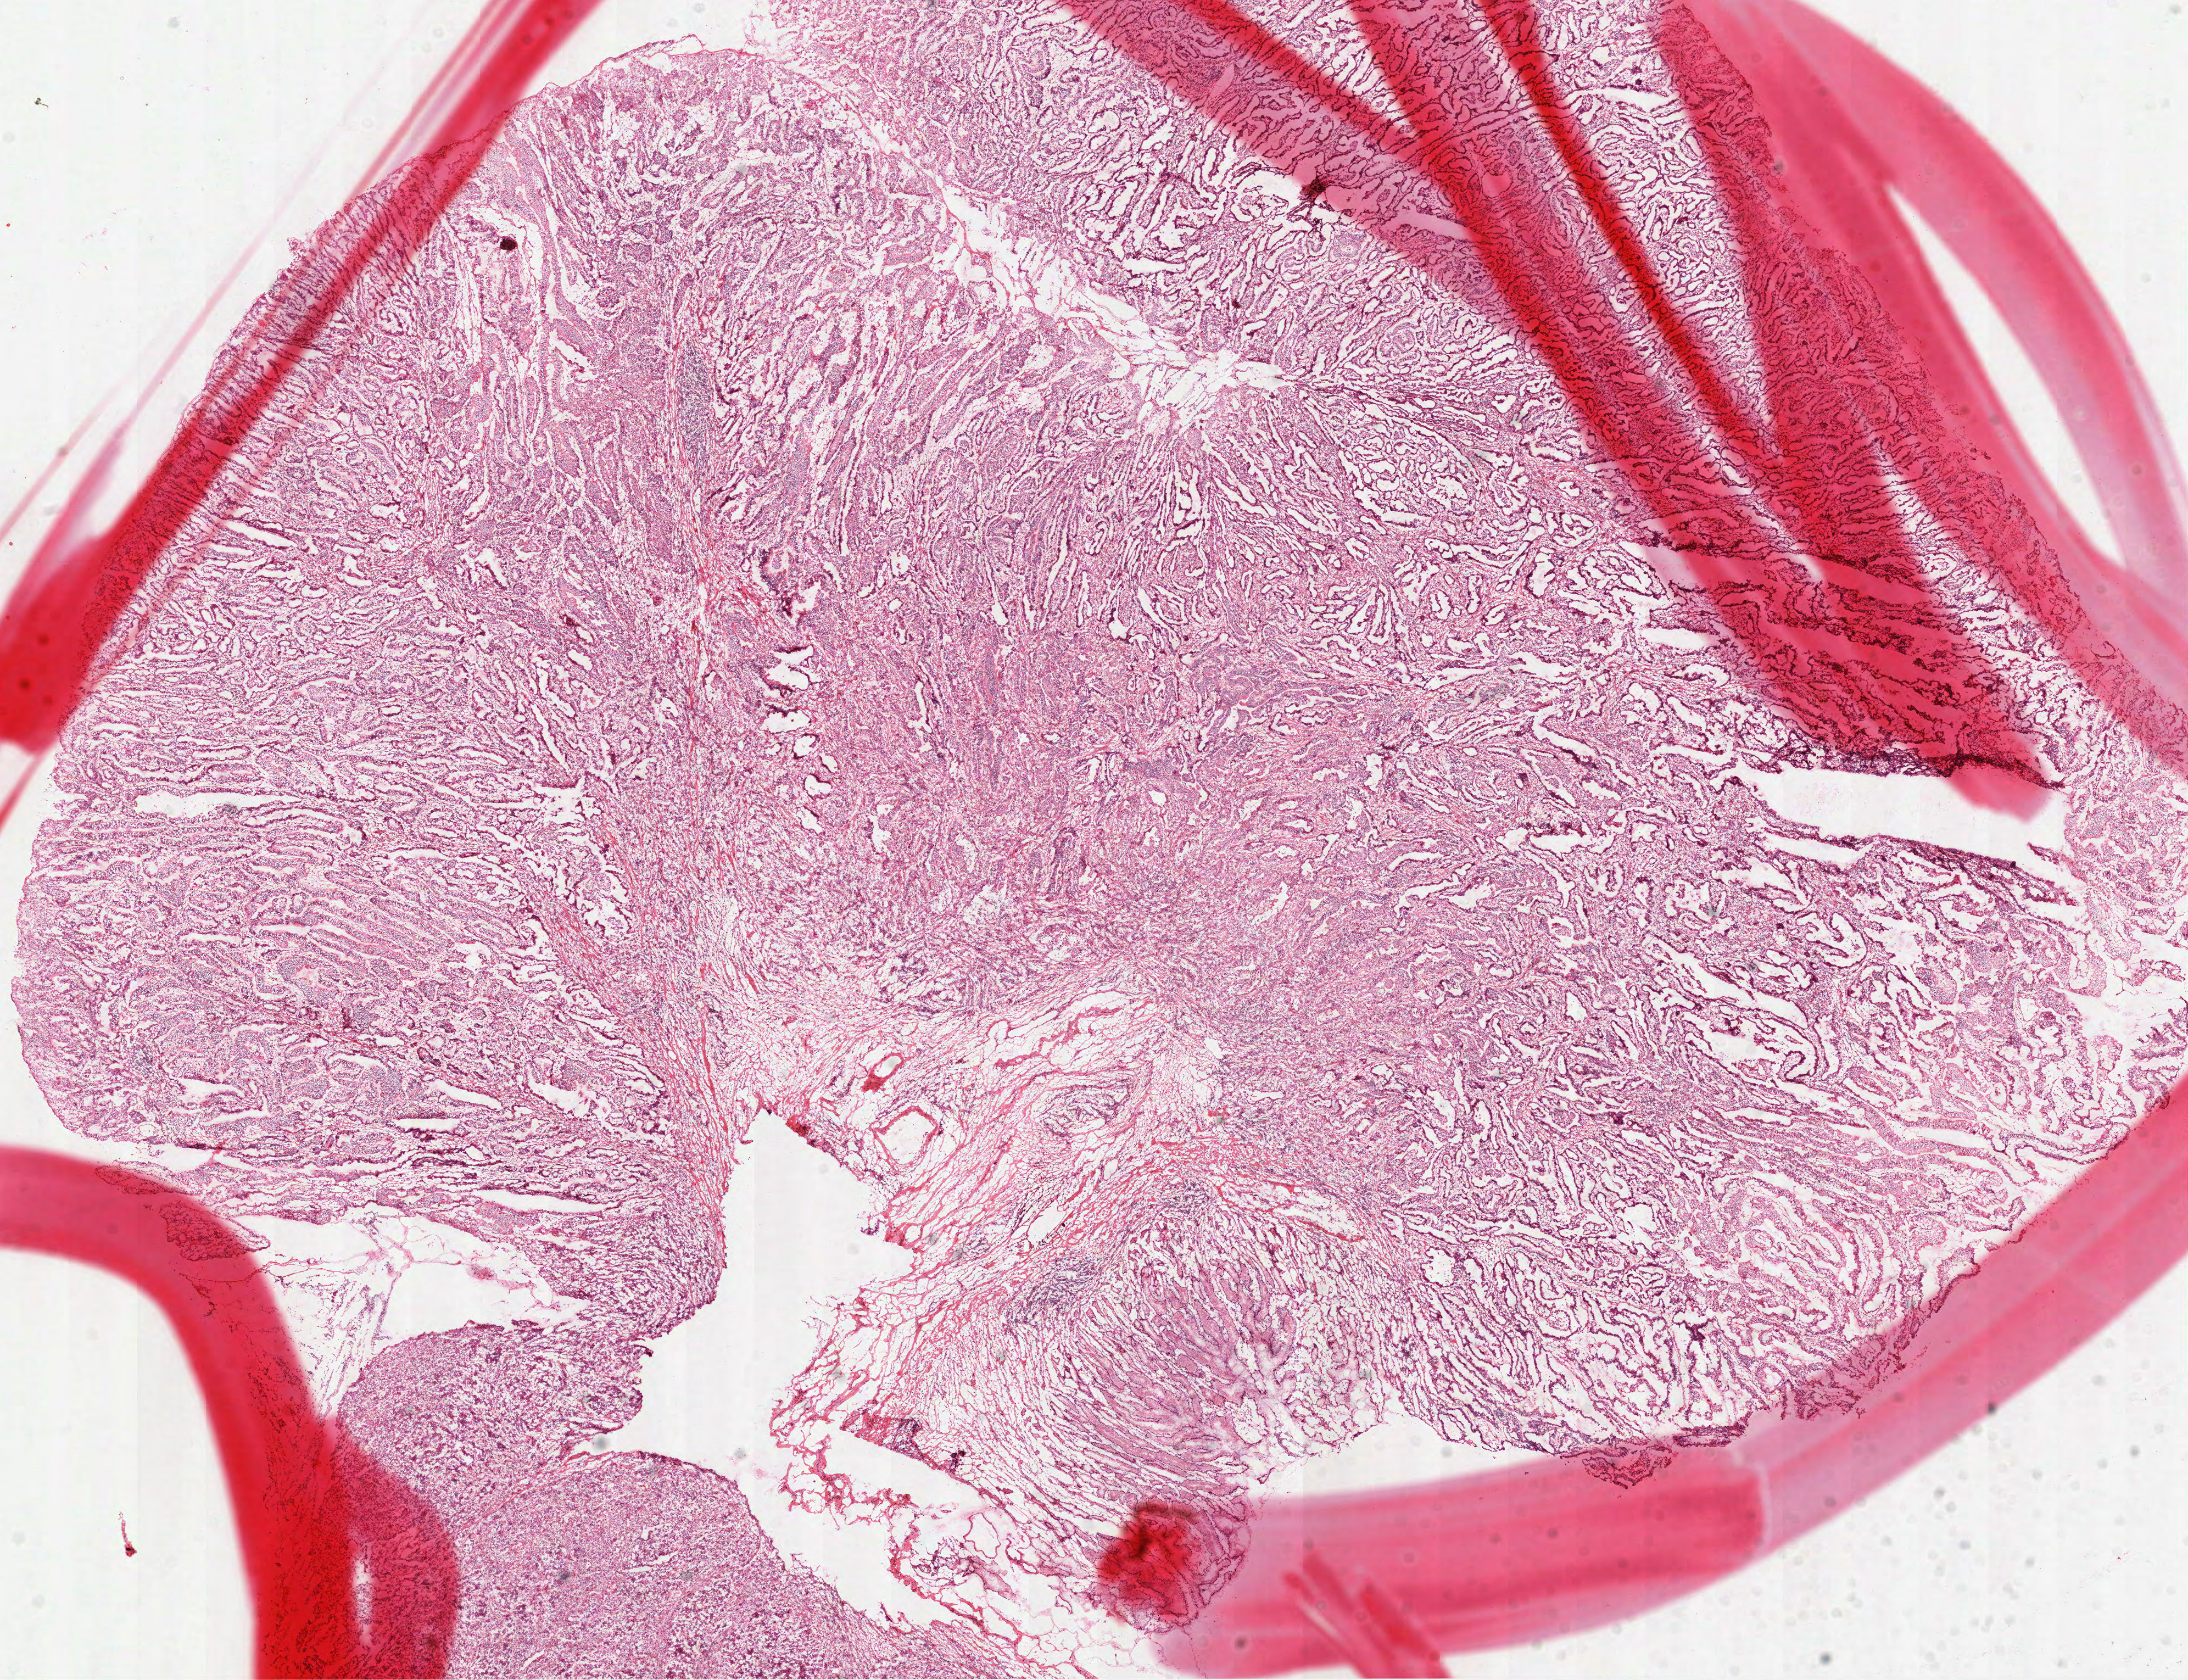
Whole-slide histology image, Hematoxylin and eosin (H&E) stained, low-resolution overview of the scanned area, about 16.1 x 12.3 mm. Frozen section from the top of the tissue portion. Stomach, primary tumour sample. Female, age 78 years at initial diagnosis. Histologic grade: G3 (poorly differentiated). Pathologist review of this section (percent, as recorded): tumour cells 100%, tumour nuclei 75%, normal cells 0%, stromal cells 0%, necrosis 0%. Infiltration values recorded for this section: lymphocyte infiltration 15%, monocyte infiltration 0%, neutrophil infiltration 2%.
- diagnosis: Adenocarcinoma, NOS
- AJCC pathologic stage: IIA (7th edition)